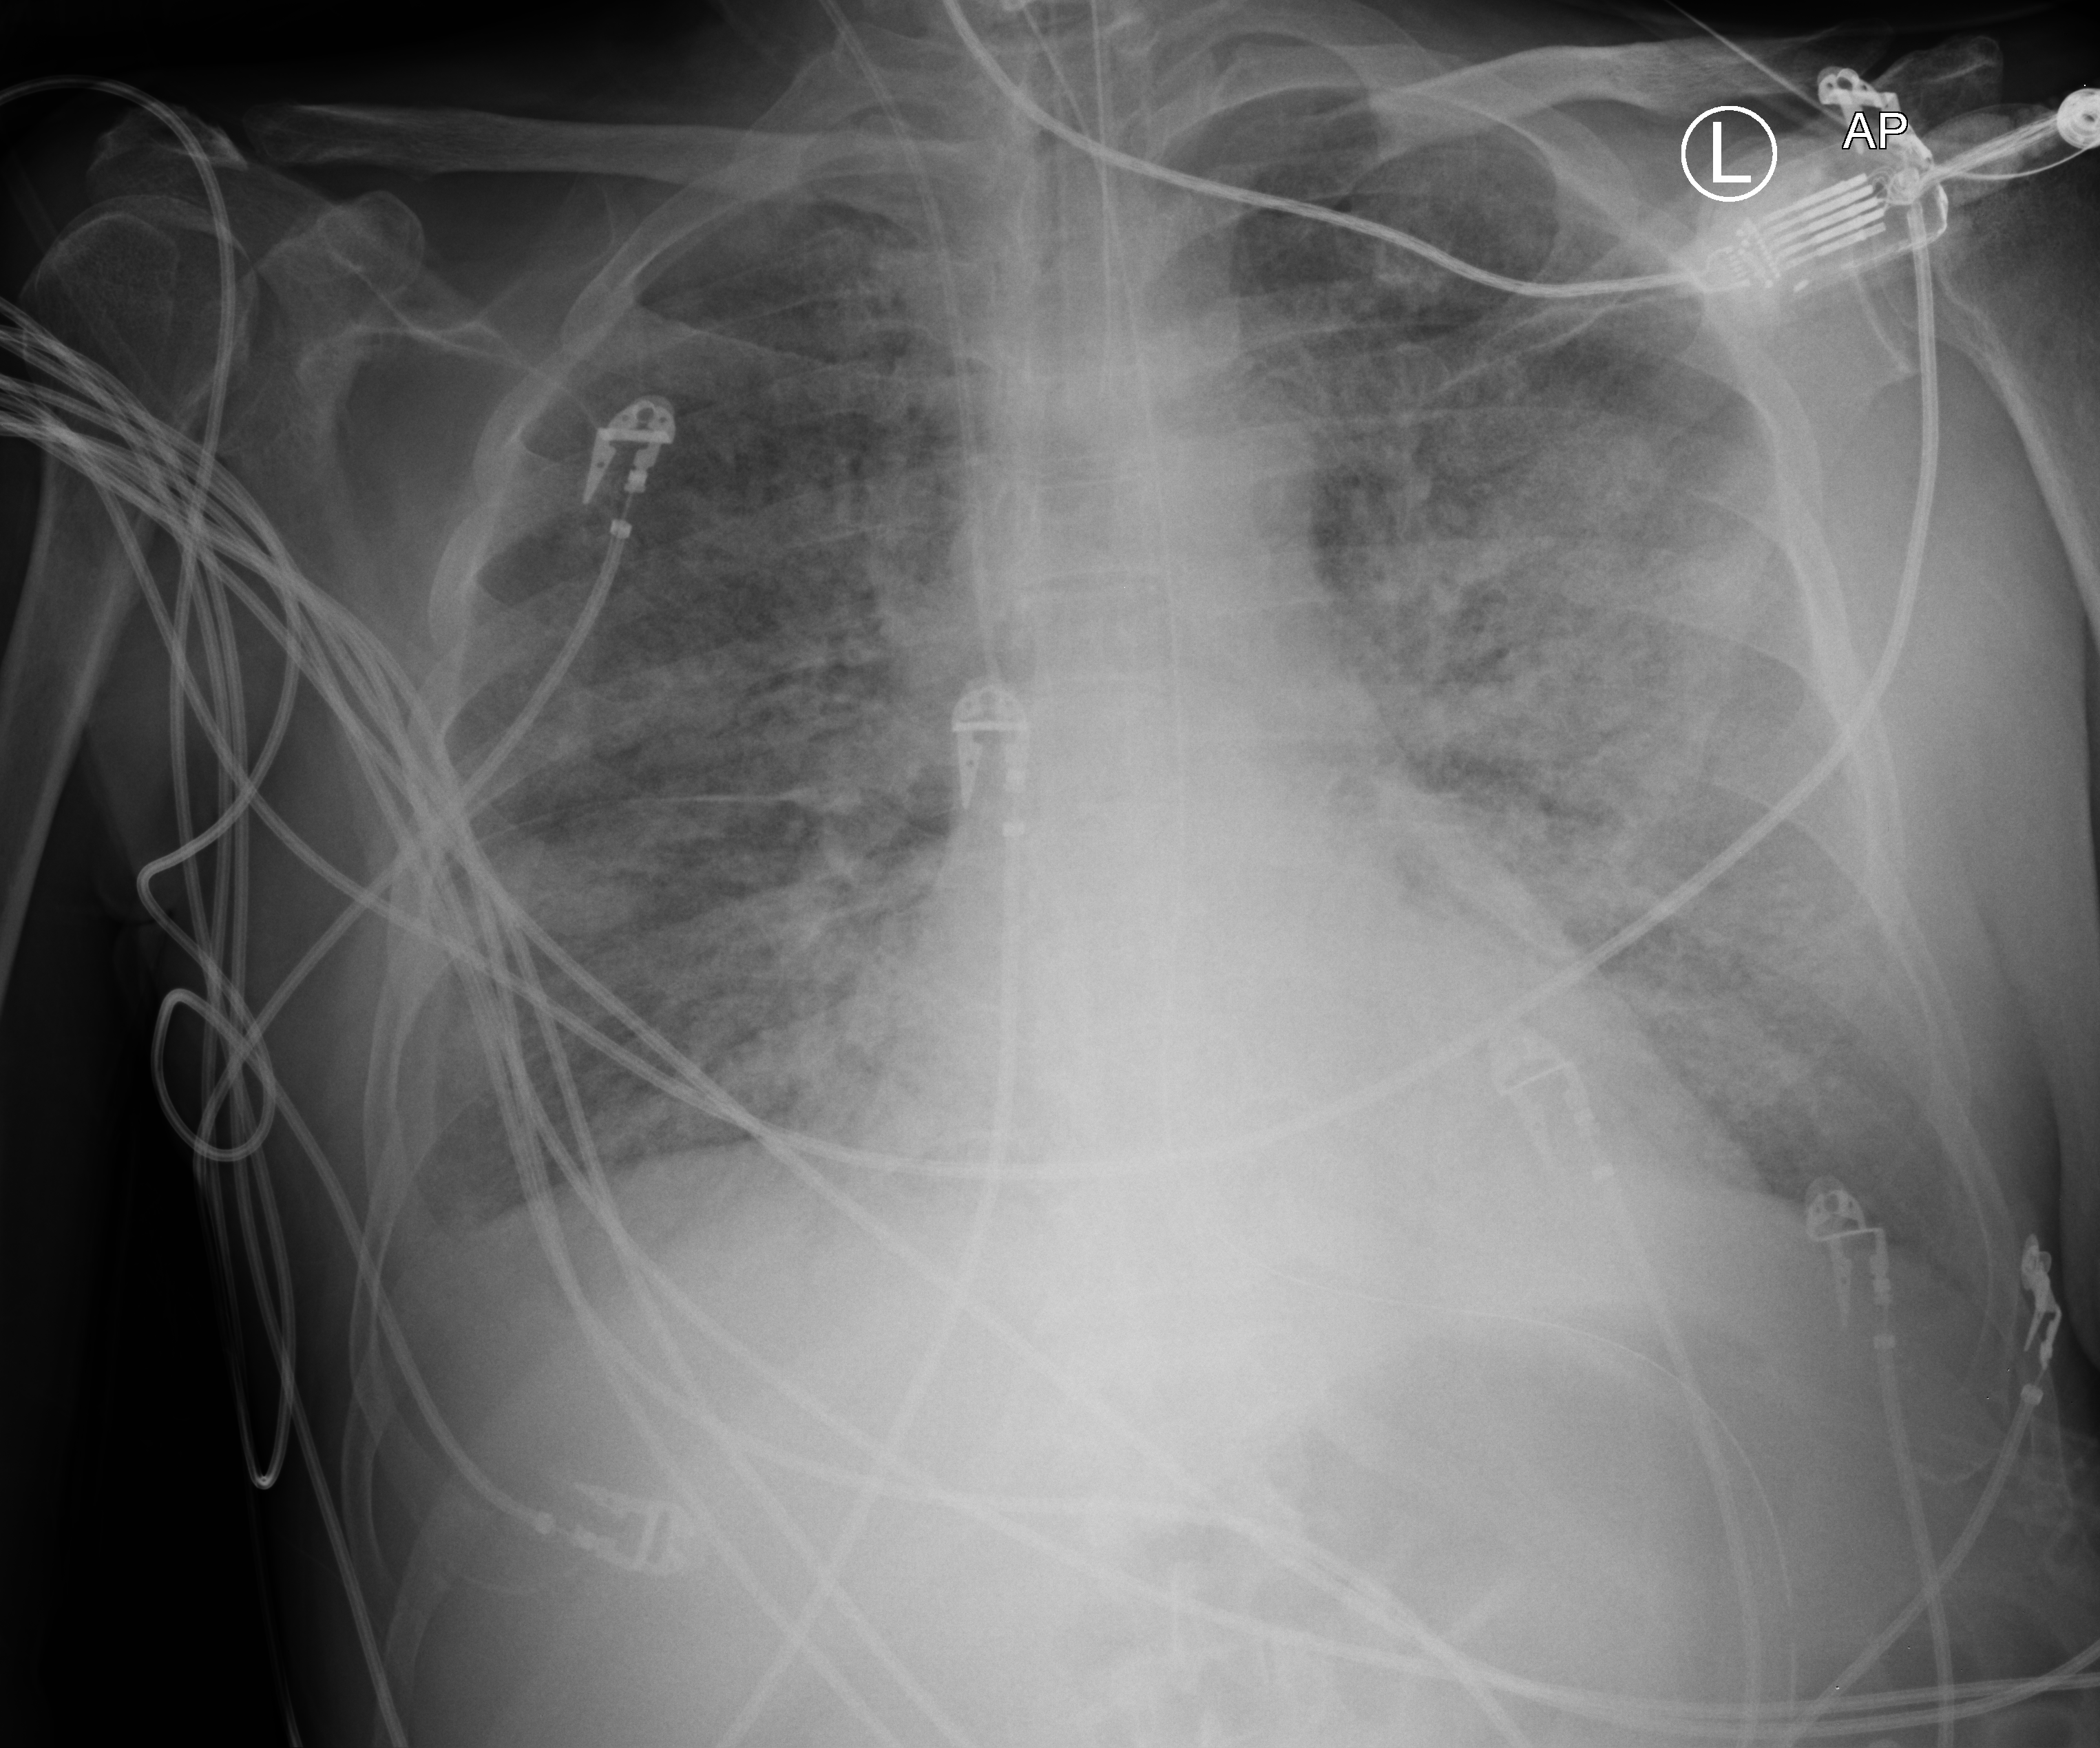
Bedside chest radiograph (computed radiography); anteroposterior (AP) projection. Male patient hospitalised with COVID-19, age 60–74 years.
Admission-level facts for this patient (not findings on this image; timing relative to this image not recorded): other chronic lung disease (admission record): no; mechanically ventilated during this hospital stay: yes; chronic kidney disease (admission record): no.